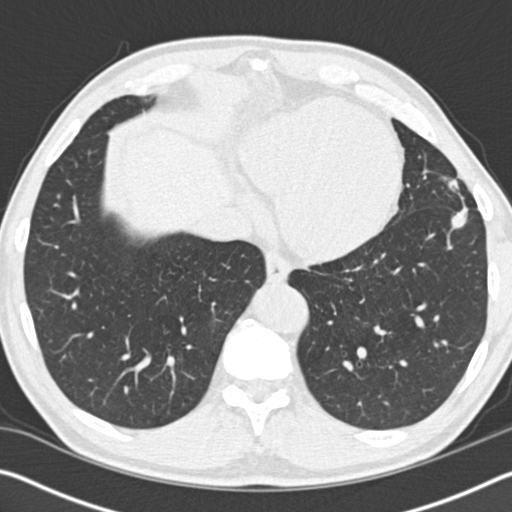
Low-dose screening chest CT, one axial slice; slice 41 of 162 in the series (ordered by position); reconstruction kernel B30f; 120 kVp; lung window (W 1500 / L -600 HU); 512 × 512 image matrix, field of view 340 × 340 mm.
Structures marked on this image (outlined manually by an expert reader):
- lesion 1 (tumor, upper lobe of left lung): bounding box <445,178,468,229> (left, top, right, bottom; pixels)